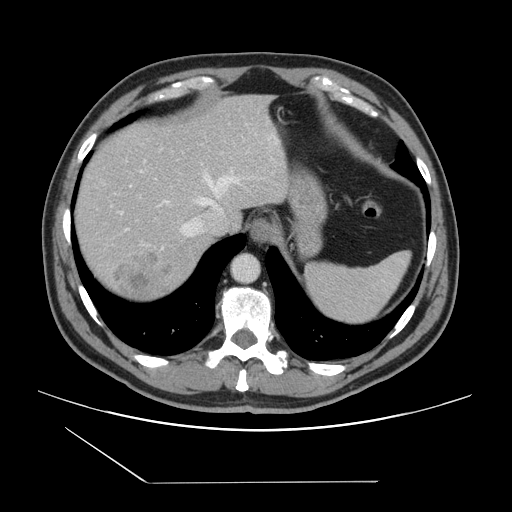
Contrast-enhanced abdominal CT, one axial slice; position 121 of 157 along the scan axis; intravenous contrast given; soft-tissue window (W 400 / L 40 HU); 2.5 mm slice thickness; 512 × 512 image matrix, field of view 407 × 407 mm. Male patient, age 61 years. Case-level facts recorded for this patient, not image findings: diagnosis: colorectal cancer liver metastases, imaged before liver resection; multiple liver metastases: yes; largest metastasis: 5.5 cm.
Annotated regions visible in this slice (outlined manually by an expert reader):
- hepatic veins: box from (x=140, y=170) to (x=240, y=250) px
- liver: (x=74, y=95)–(x=288, y=304)
- planned liver remnant (the part of the liver to remain after resection): (x=74, y=98)–(x=234, y=230)
- liver metastasis: (x=108, y=249)–(x=177, y=301)